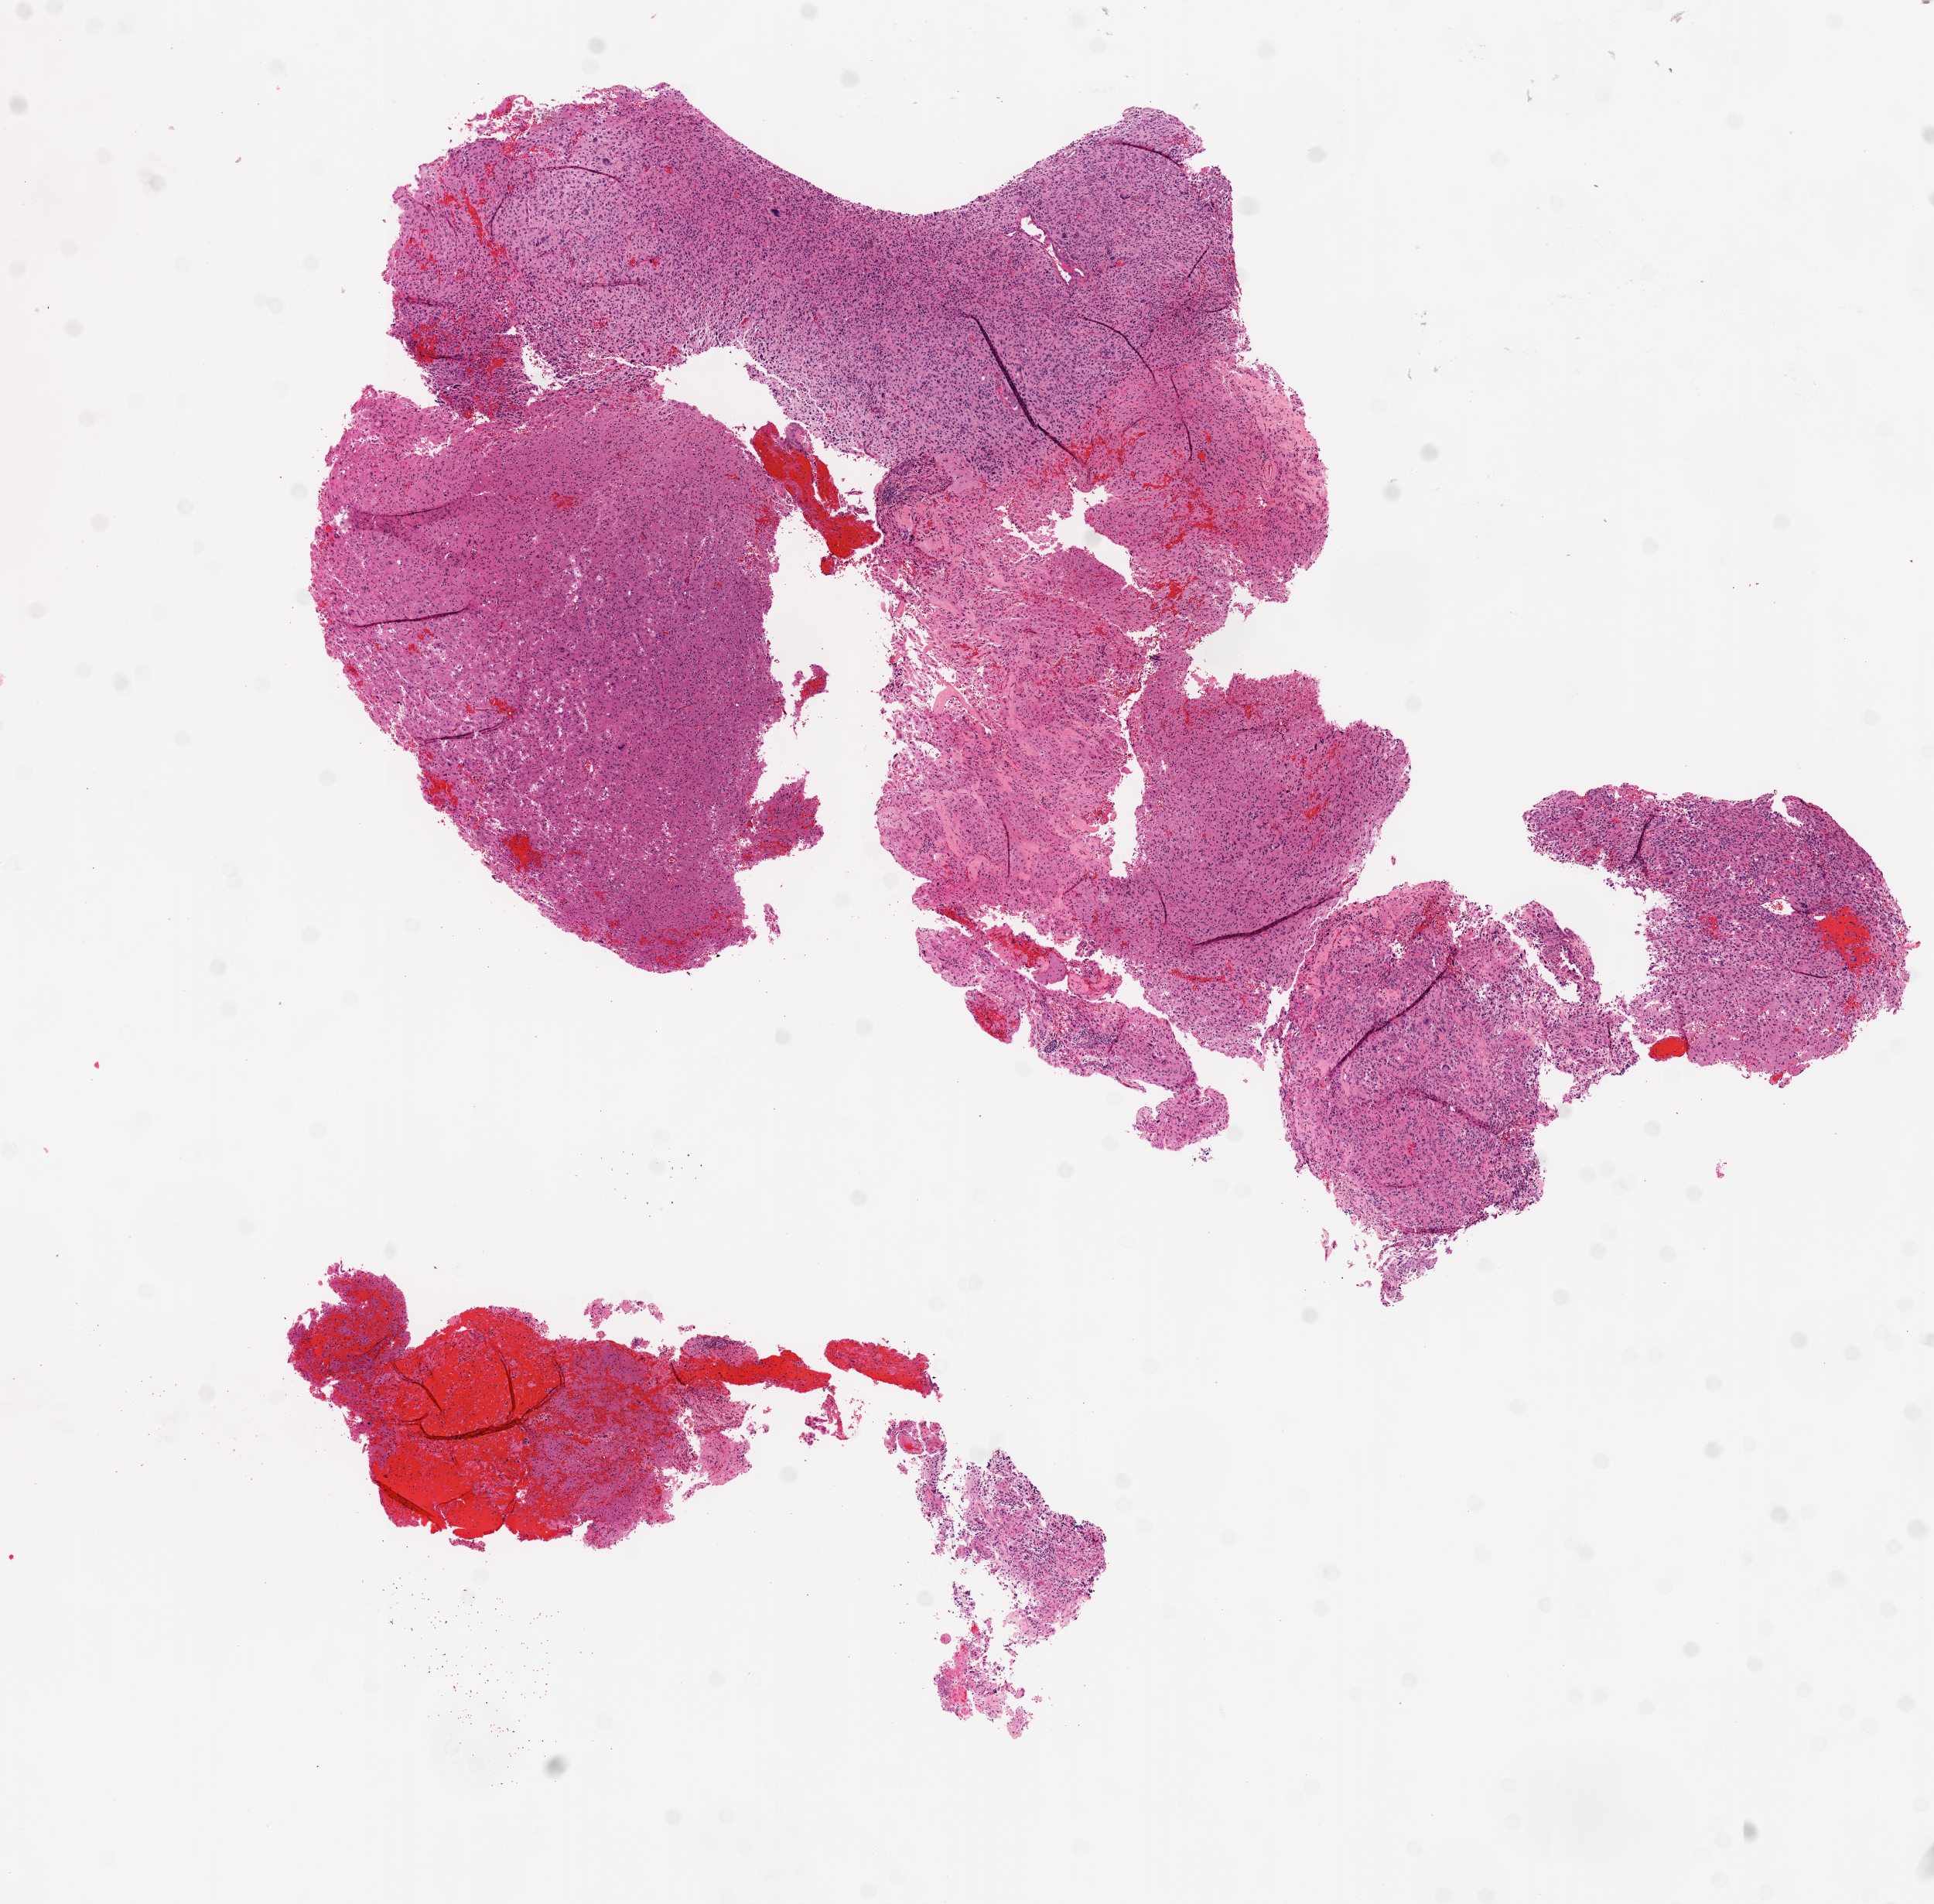
Whole-slide histology image, Hematoxylin and eosin (H&E) stained — a low-resolution overview of the entire scanned area, about 10.0 x 9.9 mm (from a 20x scan); frozen section from the top of the tissue portion; sample: primary tumour, brain. Female patient; age at initial diagnosis 47 years. Composition of this section per pathologist review: tumour cells 100%, tumour nuclei 80%, normal cells 0%, stromal cells 0%, necrosis 0%.
Pathologic diagnosis: Glioblastoma.